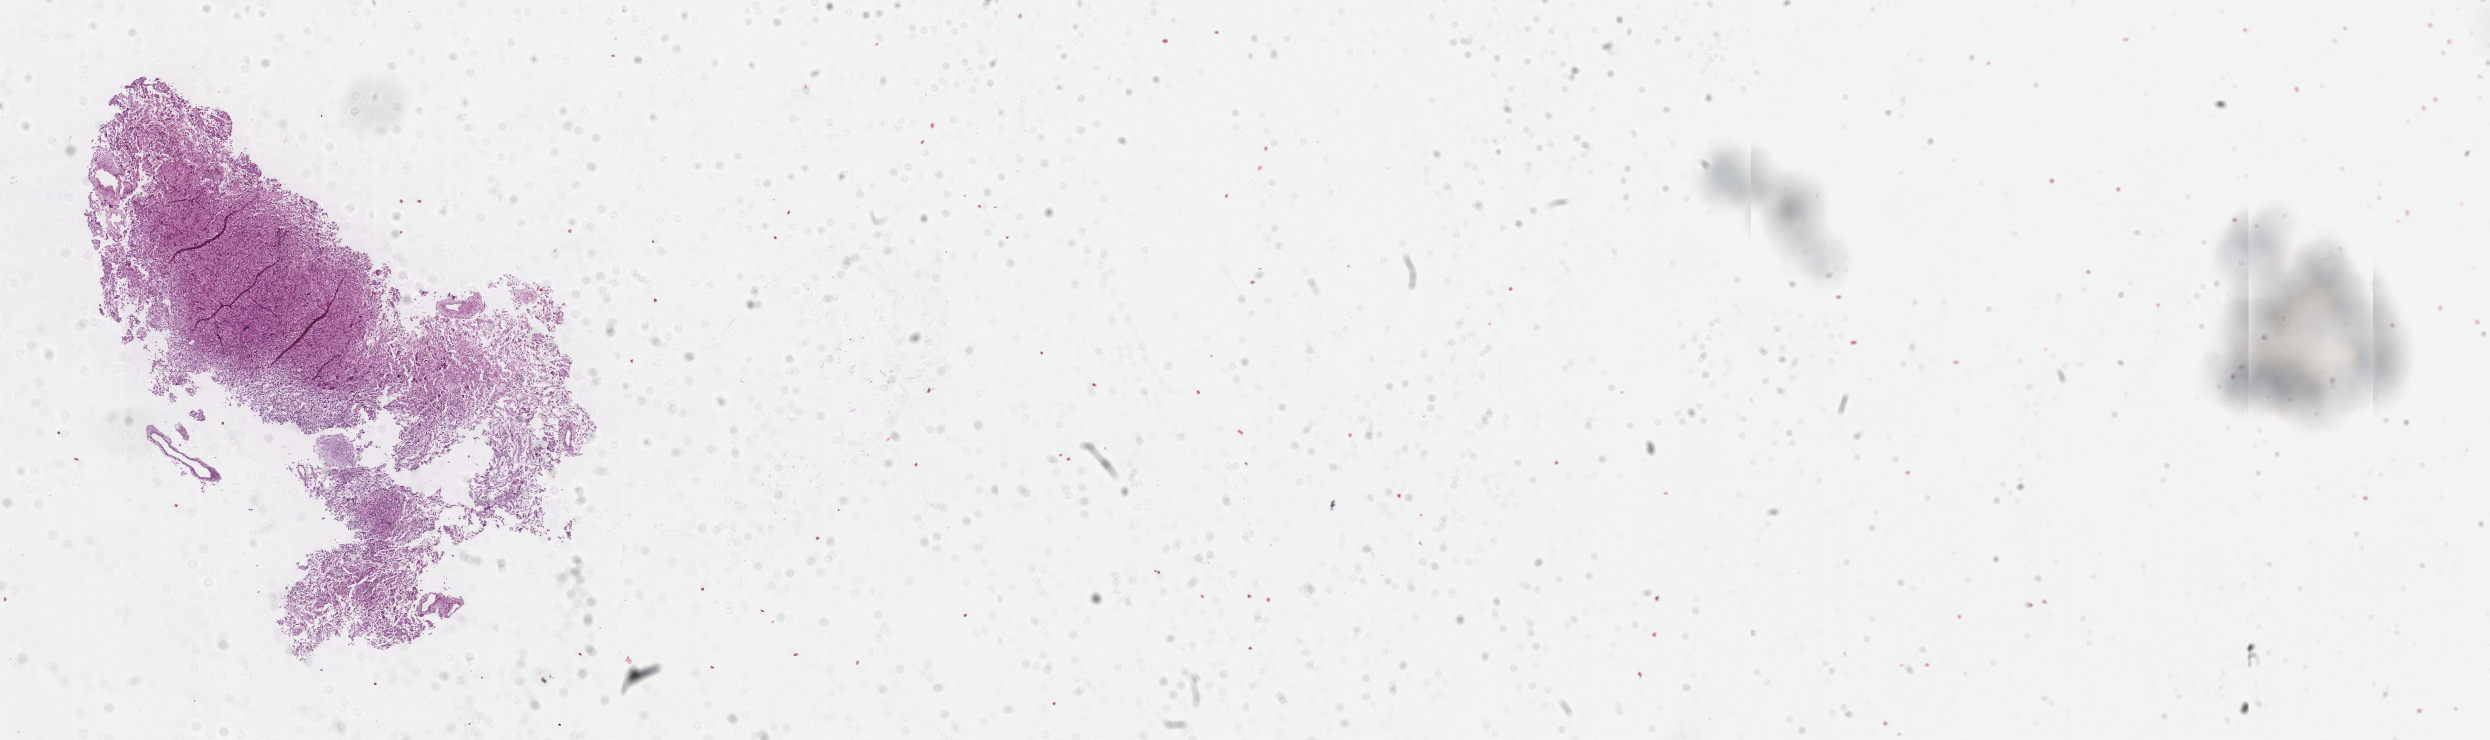
Whole-slide histology image, Hematoxylin and eosin (H&E) stained, whole scanned area (about 20.1 x 6.0 mm, slide scanned at 20x) shown as a low-resolution overview; tumour tissue sample, sampled site: frontal lobe. 31-year-old male patient. Composition of this section per pathologist review: tumour nuclei 75%, necrosis 5%.
* histologic diagnosis: Glioblastoma